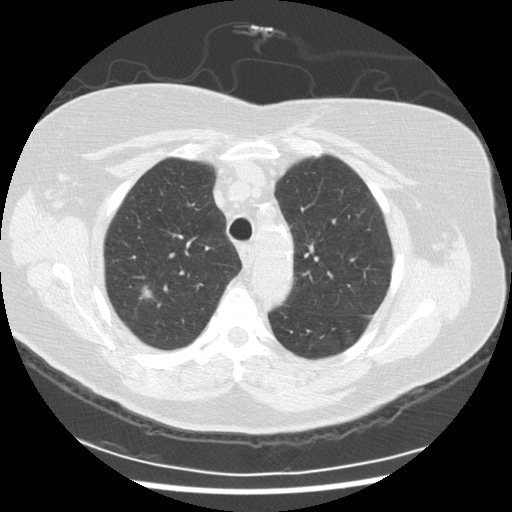
Axial slice from a low-dose chest CT screening exam. Third screening round (two years after baseline). Lung window (W 1500 / L -600 HU). Slice 53 of 254 in the series. Female, age 72 years at enrolment. Current smoker at enrolment.
• Expert-annotated lung lesion, bounding box <128,280,160,308> (left, top, right, bottom; pixels).
• Reader record for this screening exam (exam-level; its link to the box is not recorded): non-calcified nodule or mass ≥4 mm, right upper lobe, 9 × 8 mm, poorly defined margins, ground glass attenuation, pre-existing on the prior screen: no.
• Official screen result: positive, other.
• Lung cancer was diagnosed 121 days after this screen: squamous cell carcinoma, NOS, right upper lobe, poorly differentiated (G3), stage IIIA (AJCC 6th edition), 22 mm at pathology.